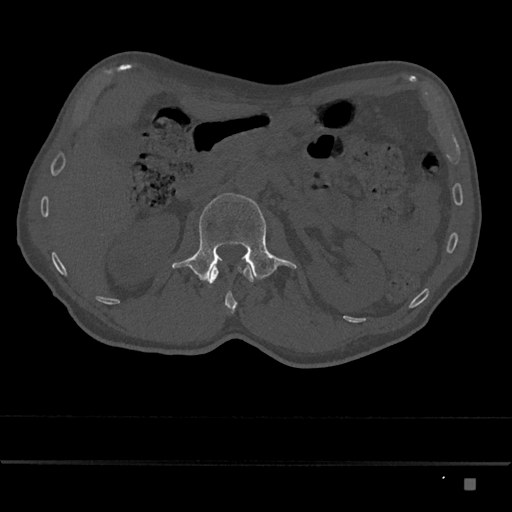
CT including the spine, one axial slice. Position 496 of 797 along the scan axis. 120 kVp. Bone window (W 1800 / L 400 HU). 512 × 512 image matrix. Patient: male, 72 years. Case-level facts recorded for this patient, not image findings: primary cancer: prostate.
Structures marked on this image (semi-automatic segmentation, software-assisted and operator-edited):
- L1 vertebra: bounding box (x1, y1, x2, y2) in pixels: (209, 264, 254, 314)
- L2 vertebra: (172, 193, 297, 282)